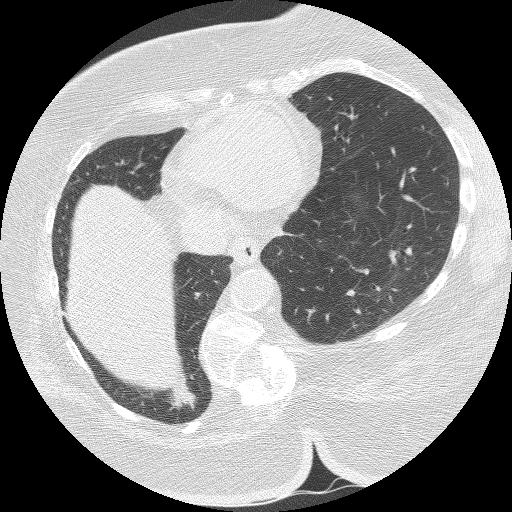
Axial slice from a low-dose chest CT screening exam, baseline annual screen, lung window (W 1500 / L -600 HU), slice 104 of 151 in the series. Female, age 59 years at enrolment.
• Expert-annotated lung lesion, box from (x=141, y=350) to (x=207, y=424) px.
• The exam's reader record, not a measurement of the box and not confirmed to be the same lesion: non-calcified nodule or mass ≥4 mm, right lower lobe, 21 × 10 mm, spiculated (stellate) margins, soft tissue attenuation.
• Official screen result: positive, change unspecified: nodule(s) >= 4 mm or enlarging nodule(s), mass(es), or other non-specific abnormalities suspicious for lung cancer.
• Later outcome: lung cancer diagnosed 52 days after this screen — bronchiolo-alveolar carcinoma, mucinous, right lower lobe, well differentiated (G1), stage IA (AJCC 6th edition), 15 mm at pathology.